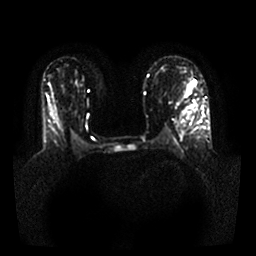
Breast MRI, one axial slice. Position 20 of 25 along the scan axis. Diffusion-weighted series; image 2 of 4 stored at this slice position (different b-values; order by instance number). 1.5 T. 256 × 256 image matrix, field of view 340 × 340 mm. Female patient.
Outlined on this slice (manually delineated by an expert):
- tumour on diffusion-weighted imaging: bounding box <192,81,196,85> (left, top, right, bottom; pixels)